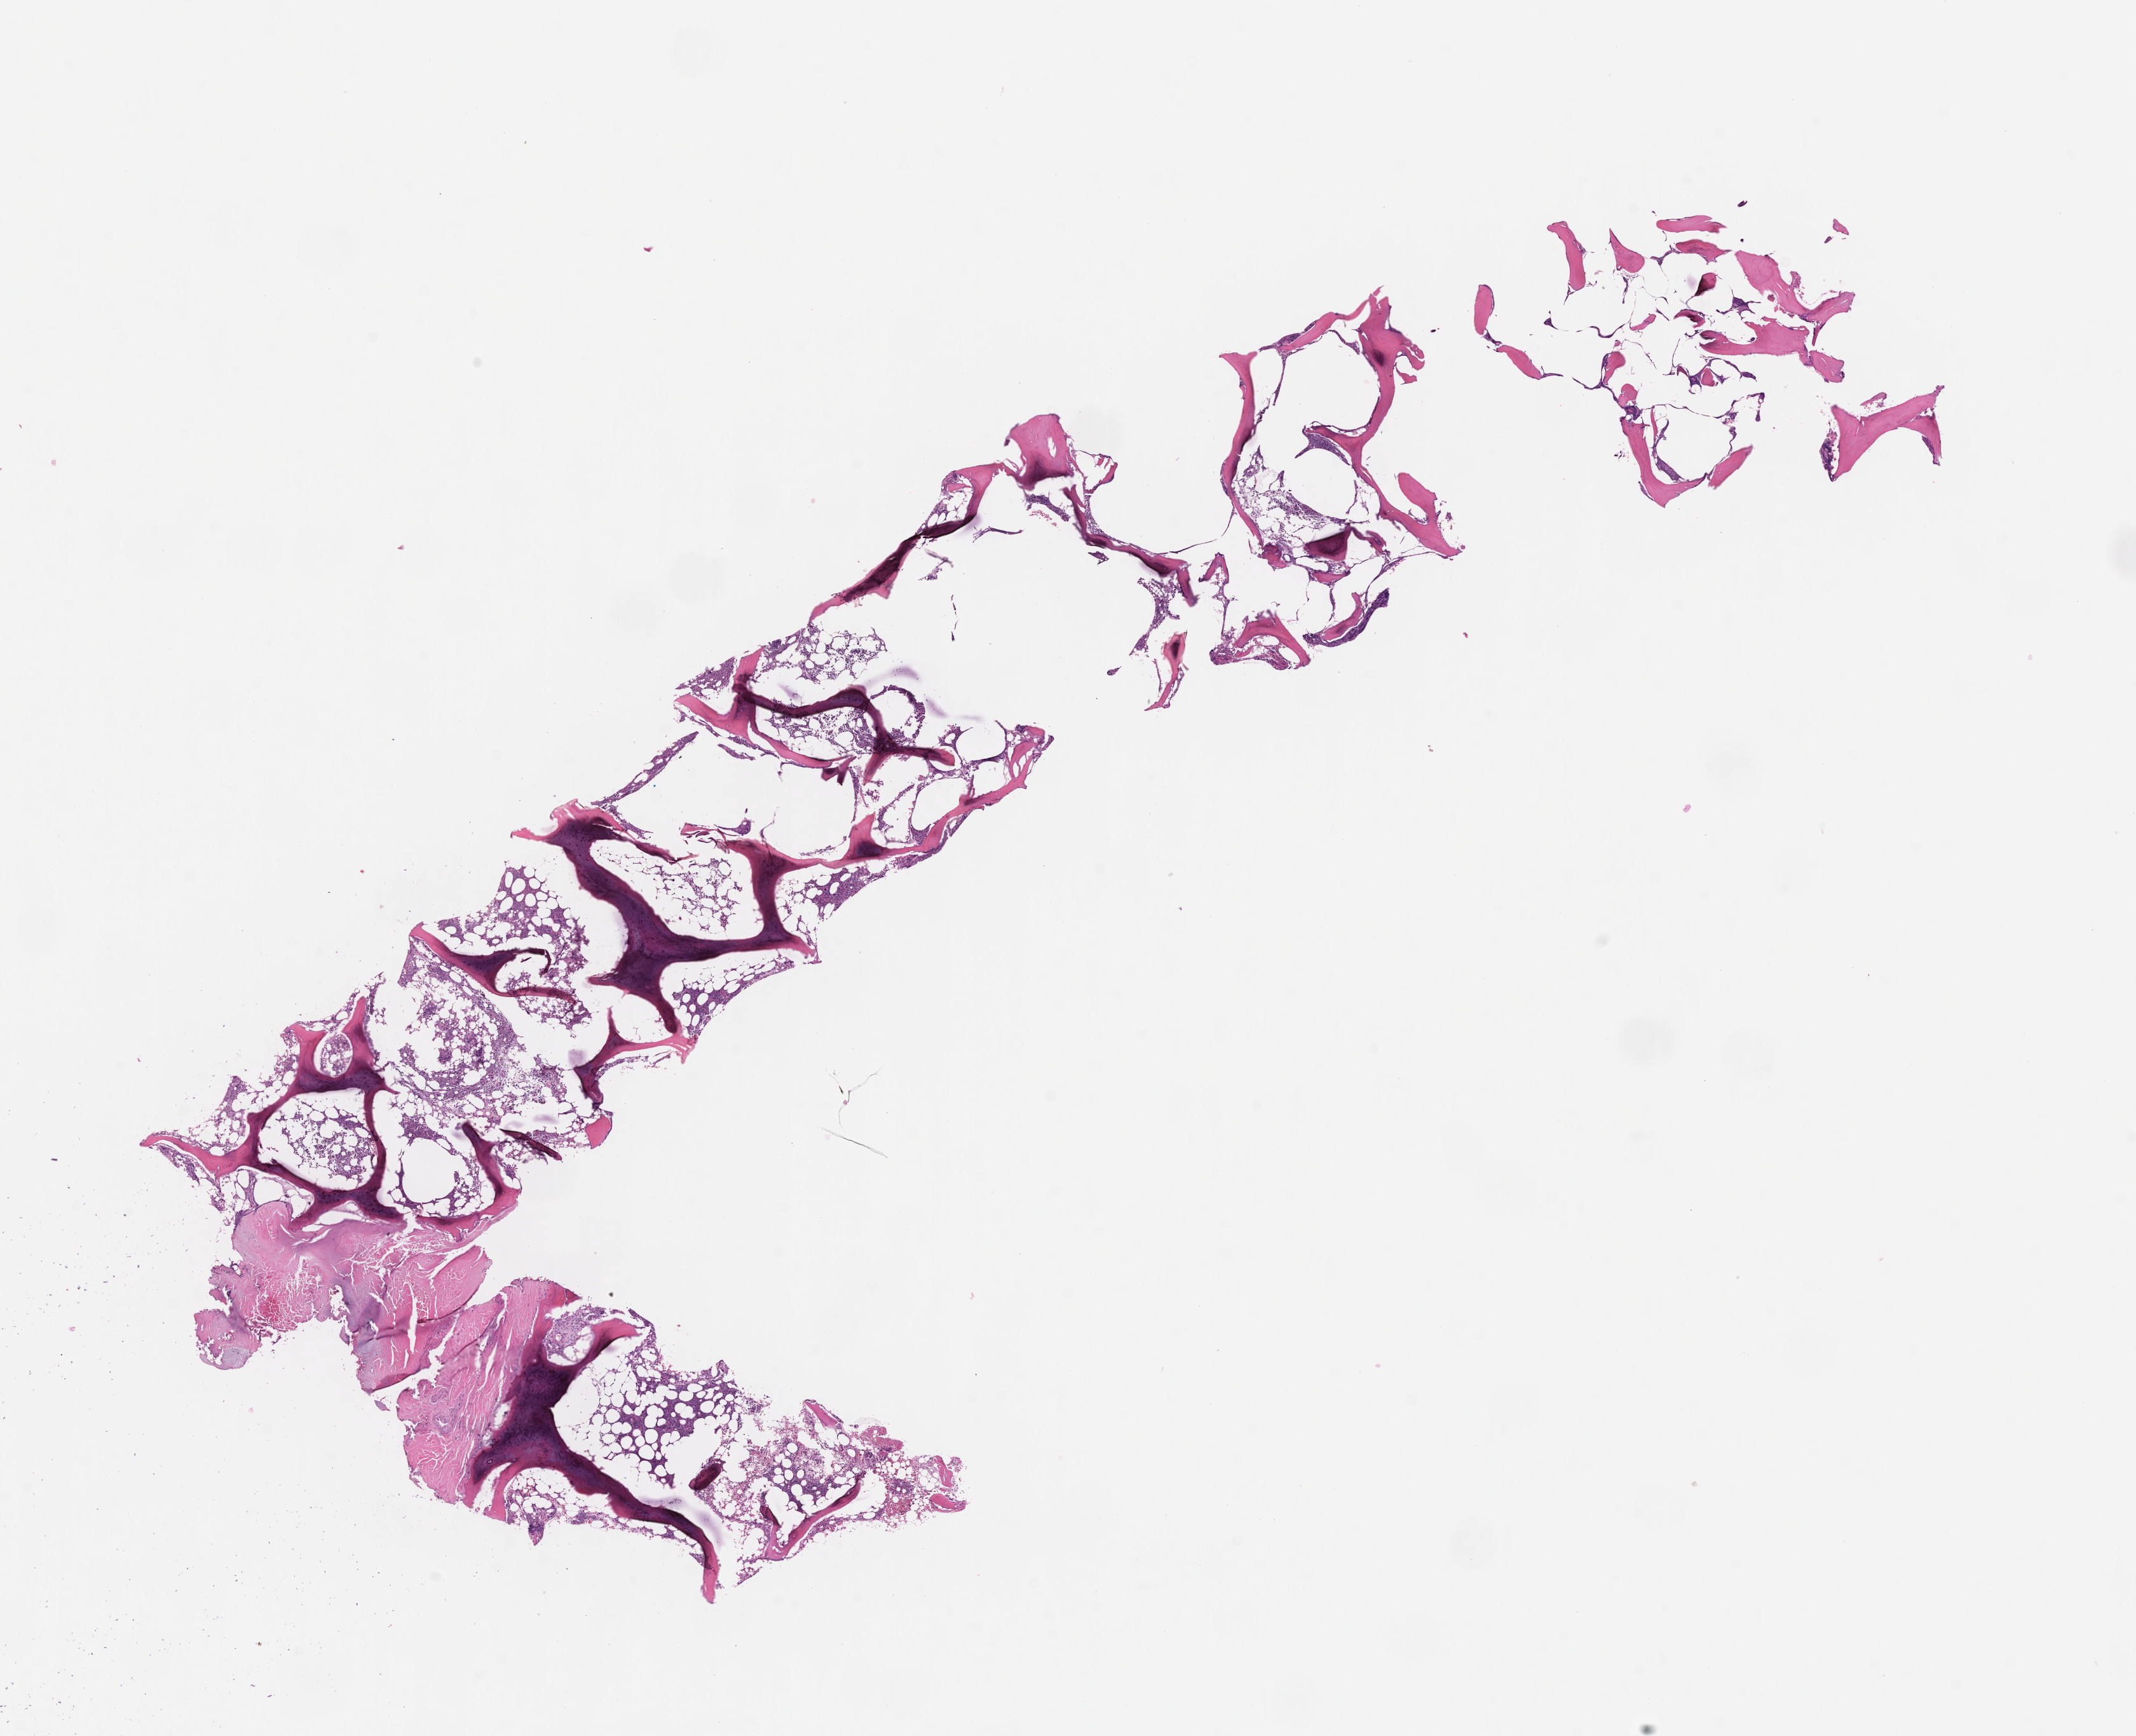
Whole-slide image, haematoxylin and eosin stain — shown as a low-resolution overview of the whole scanned area (about 13.6 x 11.0 mm). FFPE section. Tissue site: bone marrow. Specimen time point: archival tissue. Patient: male.
This section: primary tumour tissue. Diagnosis: Plasma Cell Myeloma.